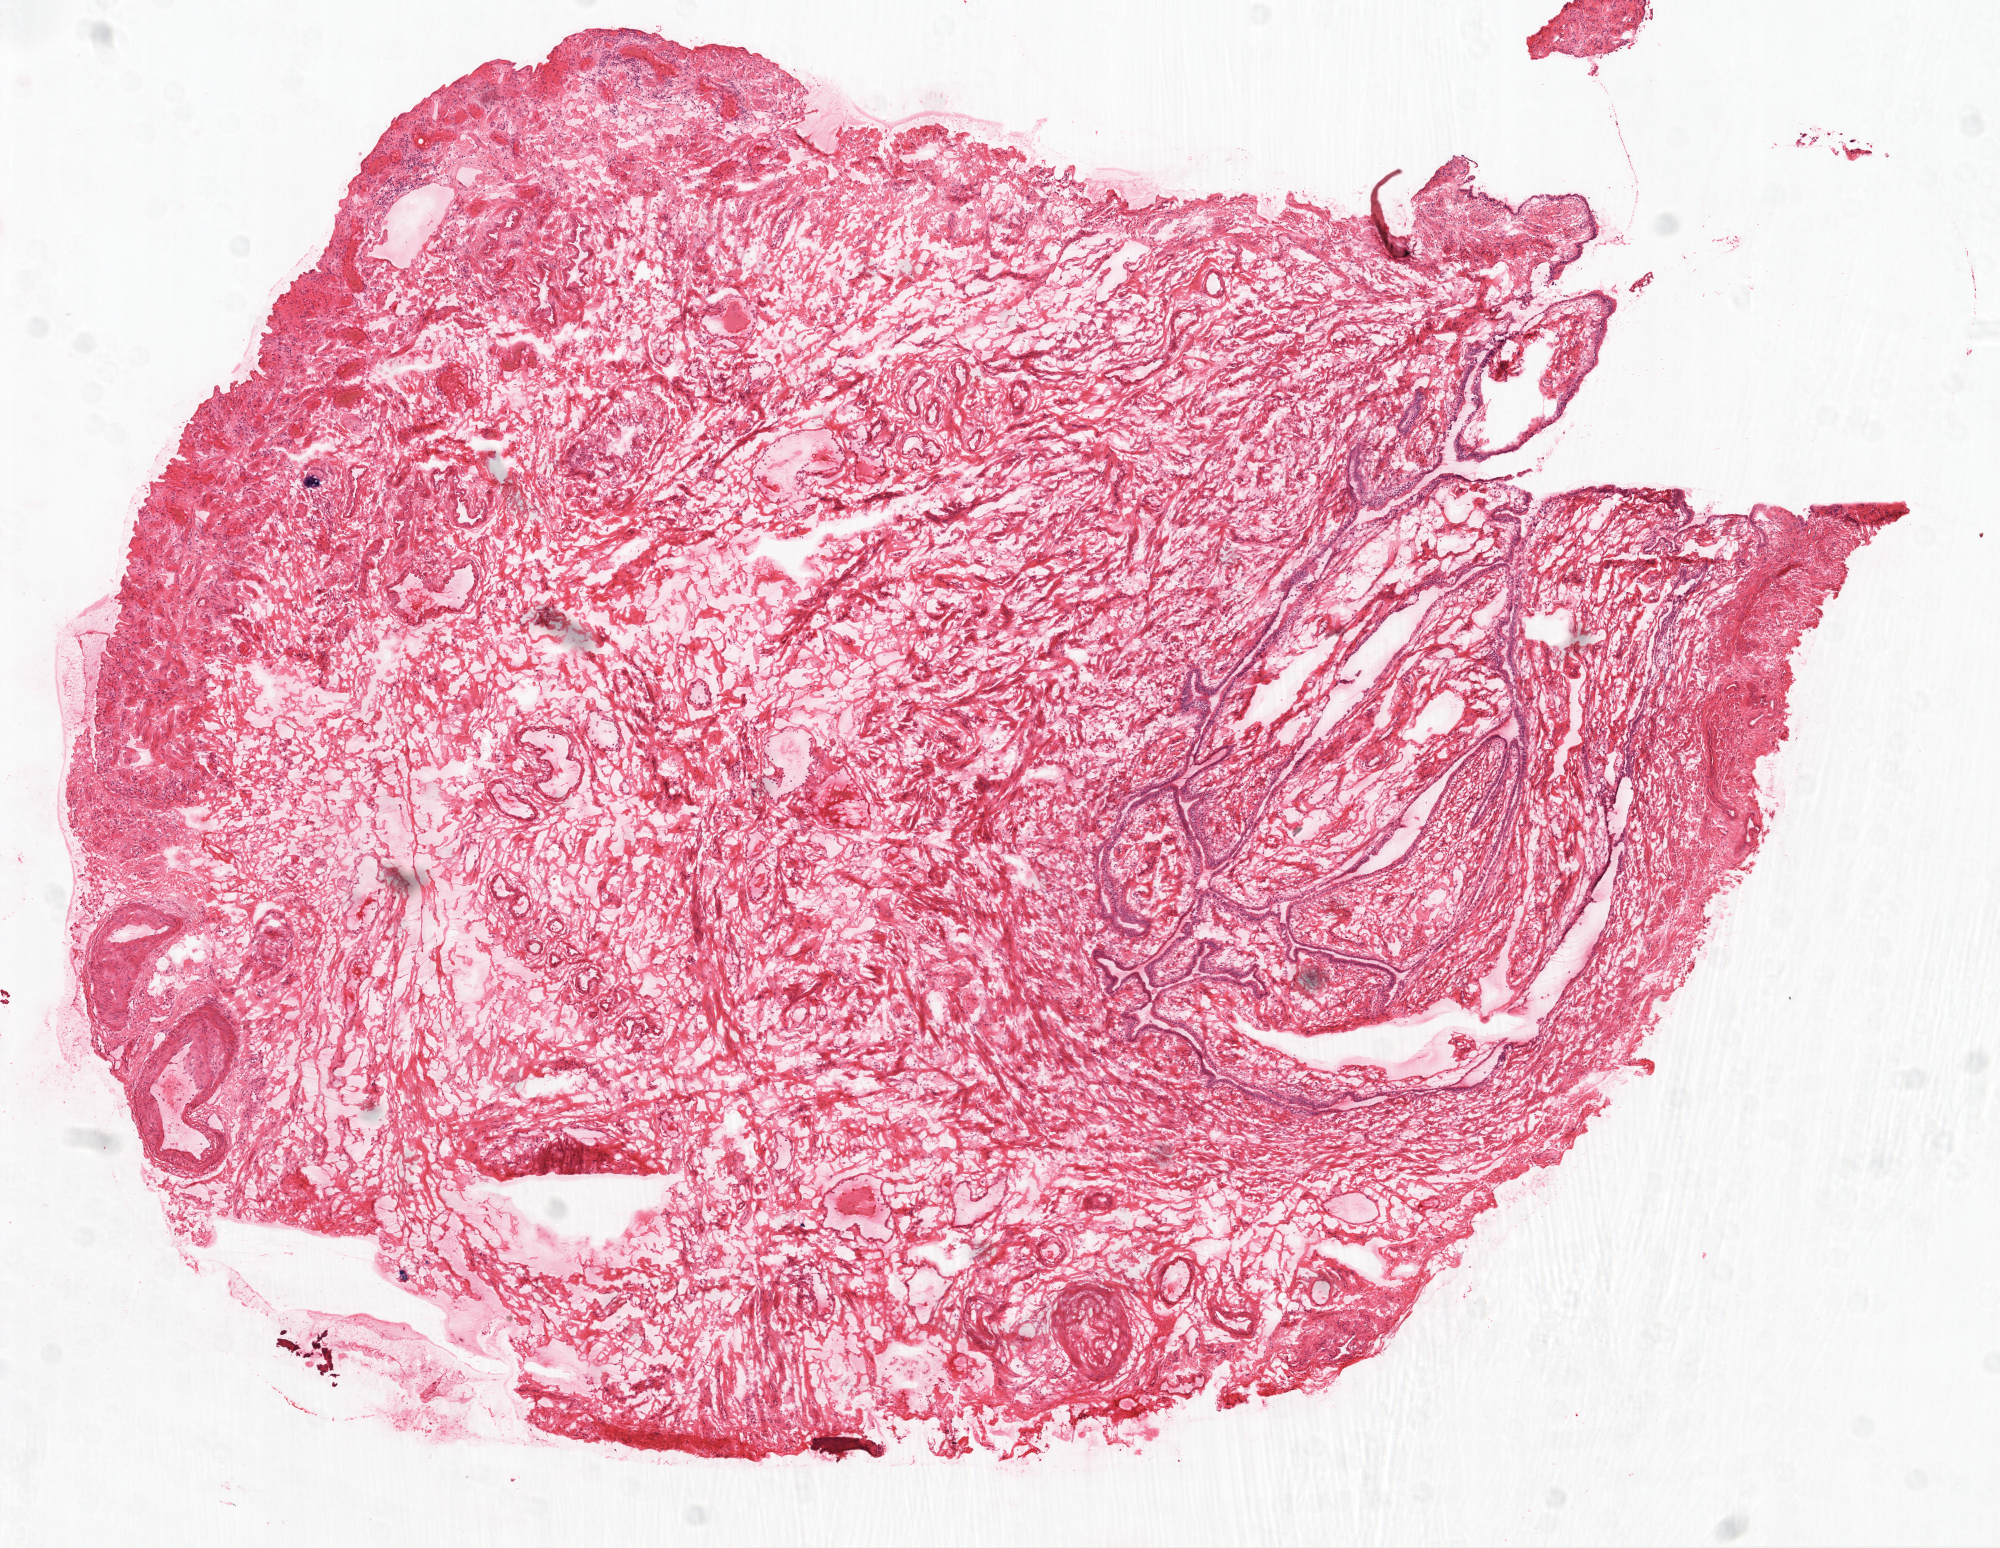
Whole-slide histology image, H&E-stained — shown as a low-resolution overview of the whole scanned area (about 8.0 x 6.2 mm); frozen section from the top of the tissue portion; ovary, solid tissue normal (non-tumour tissue) sample. Female, age 60 years at initial diagnosis.
• this section: solid tissue normal sample (biorepository sample class)
• patient diagnosis: Serous cystadenocarcinoma, NOS